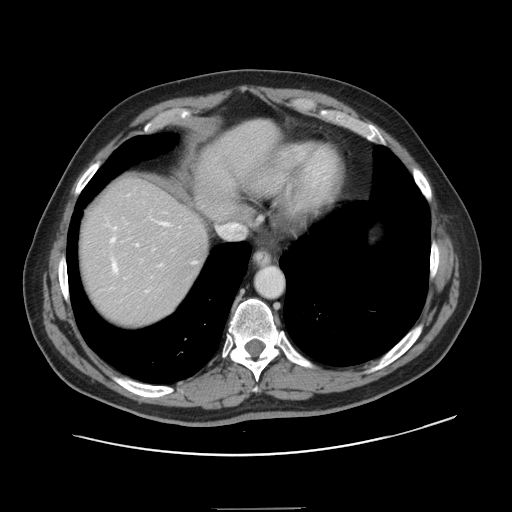
Contrast-enhanced abdominal CT, one axial slice; slice 127 of 143 in the series (ordered by position); 120 kVp; soft-tissue window (W 400 / L 40 HU); 2.5 mm slice thickness; 512 × 512 image matrix, field of view 402 × 402 mm. Male patient, age 62 years. Case-level facts recorded for this patient, not image findings: diagnosis: colorectal cancer liver metastases, imaged before liver resection; multiple liver metastases: yes; largest metastasis: 2.7 cm; disease in both lobes: no.
Outlined on this slice (outlined manually by an expert reader):
- hepatic veins: bounding box (x1, y1, x2, y2) in pixels: (111, 222, 196, 293)
- liver: (79, 120, 278, 326)
- planned liver remnant (the part of the liver to remain after resection): (79, 120, 277, 298)